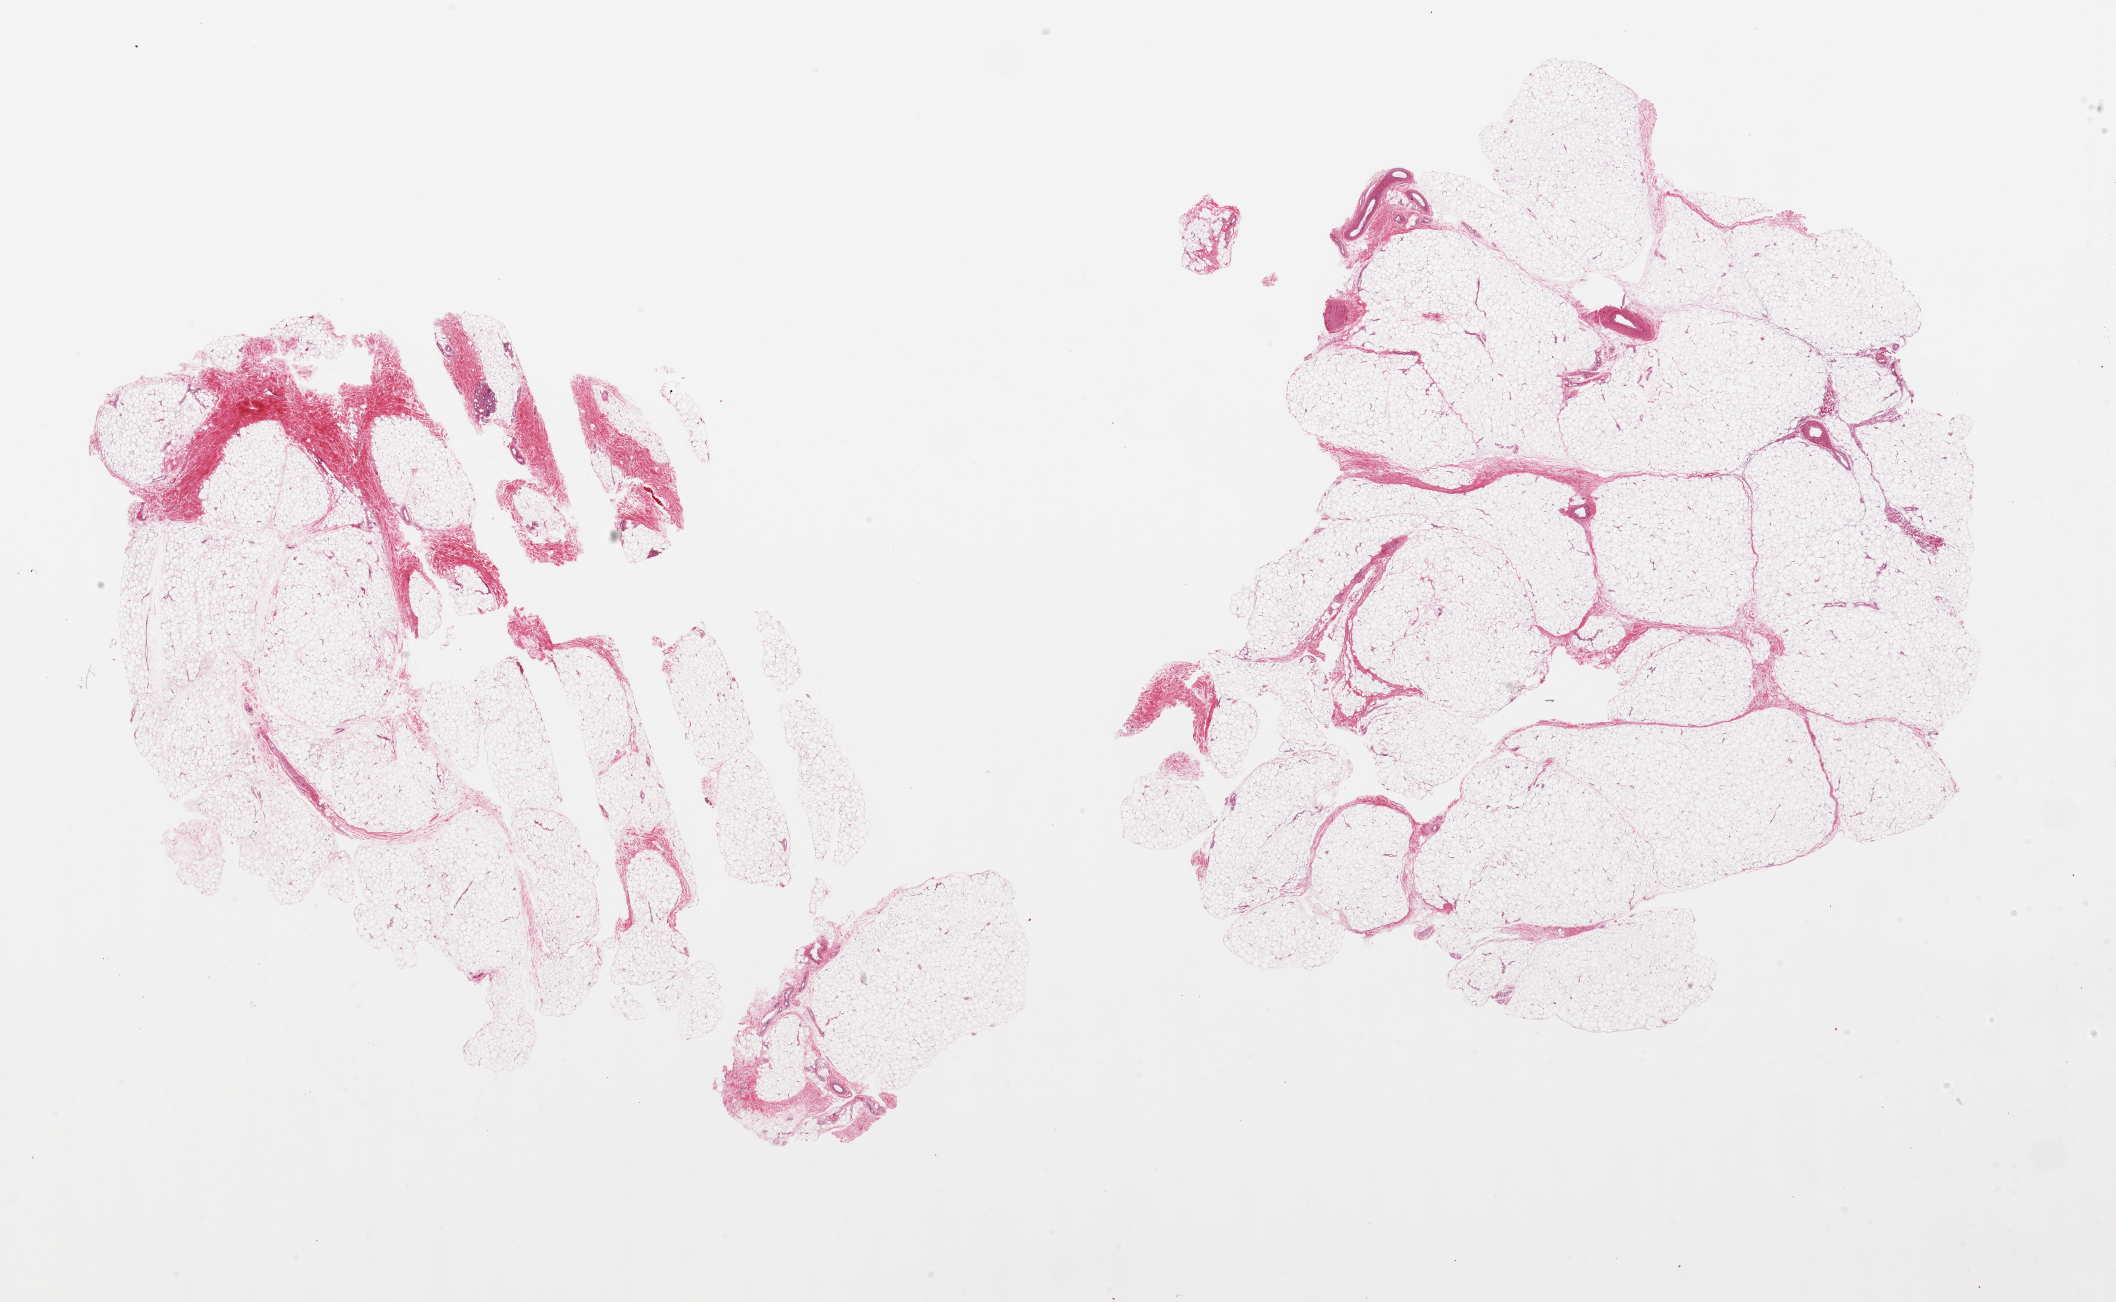
Digitized haematoxylin and eosin-stained section, brightfield — low-resolution overview of the scanned area, about 33.5 x 20.6 mm. PAXgene-fixed, paraffin-embedded tissue. Sampled site (target tissue): adipose tissue. Tissue donor sample. Male donor.
Review note (as recorded): 2 pieces. Large aliquots, some holes.